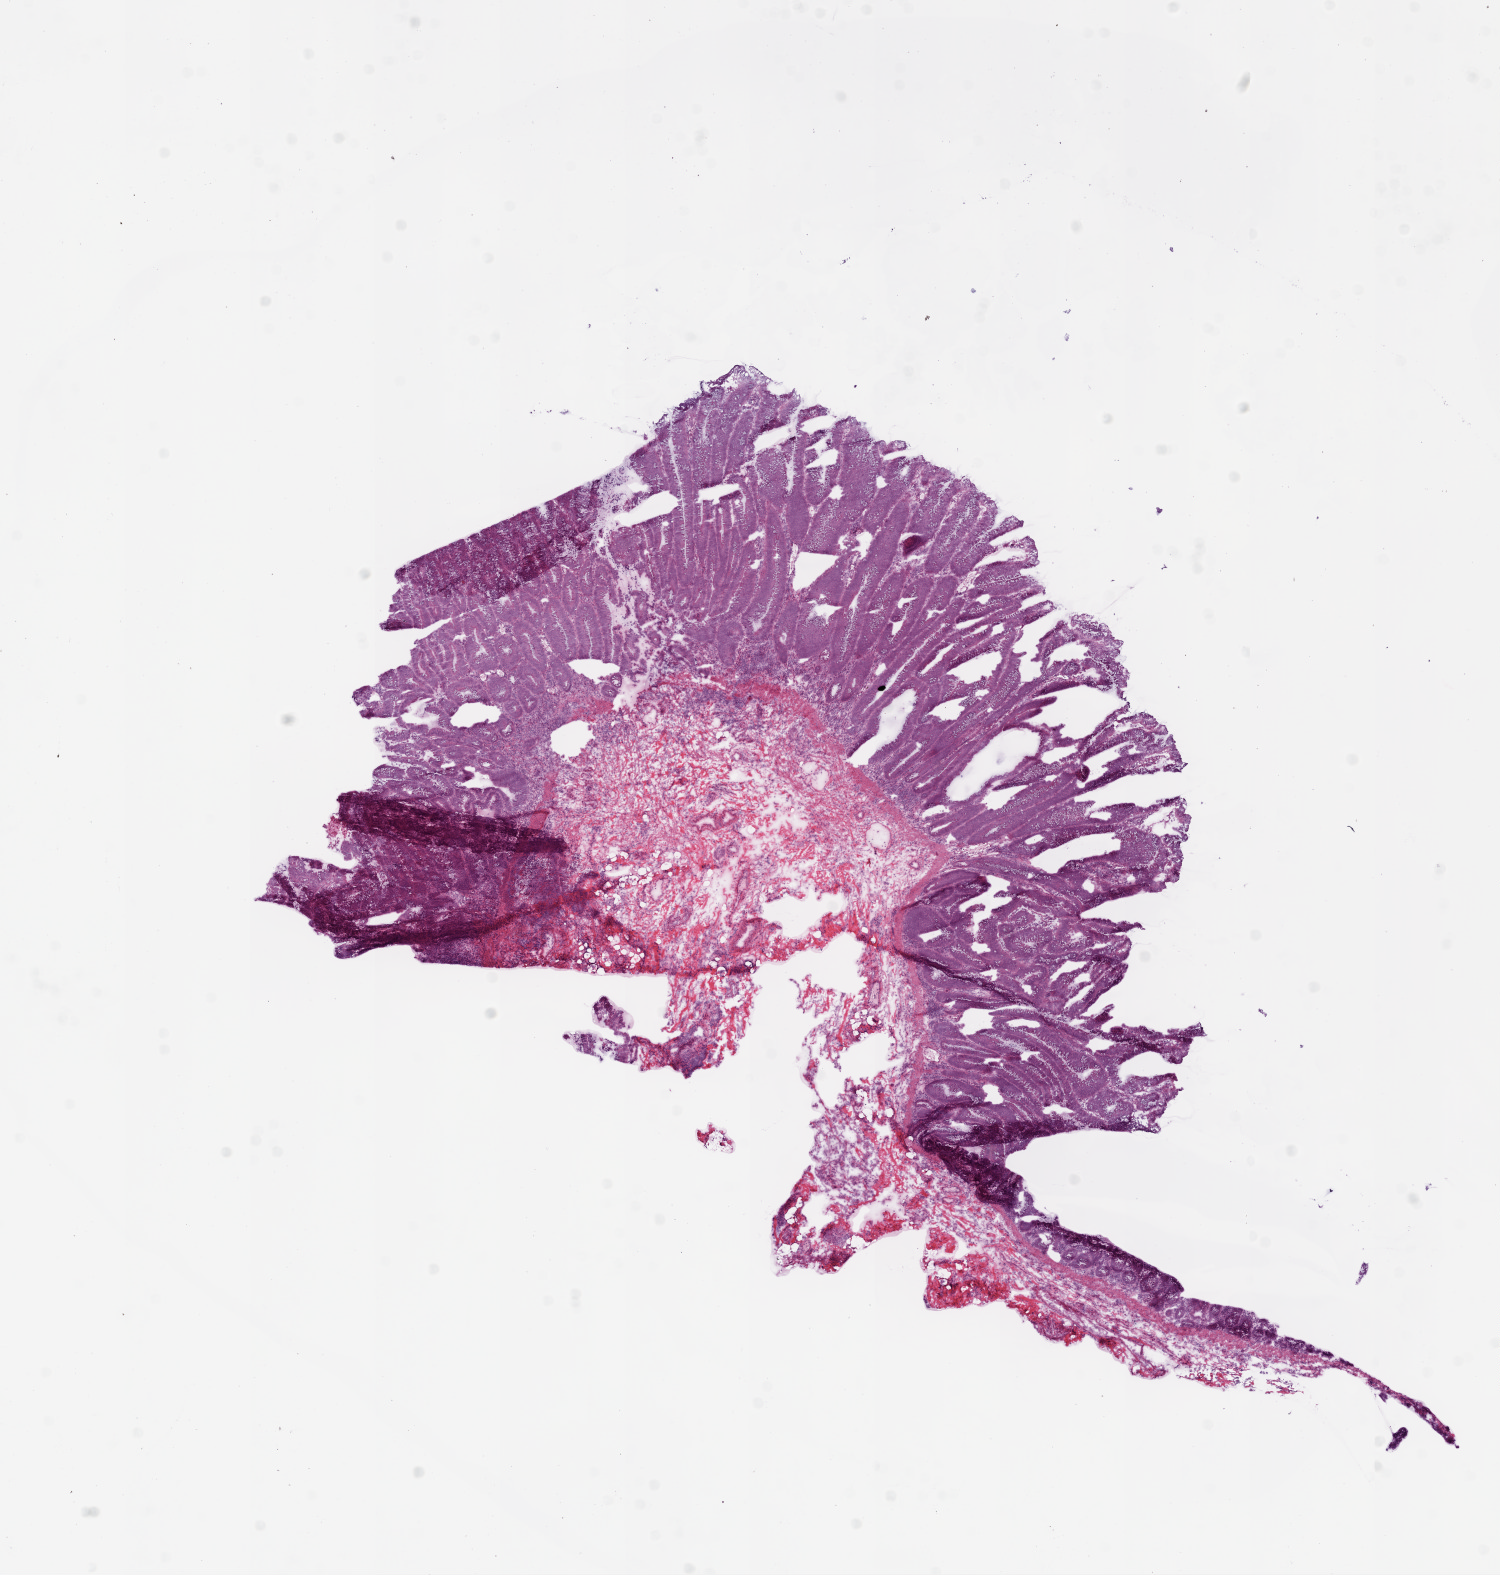
Whole-slide histology image, H&E — a low-resolution overview of the entire scanned area, about 12.0 x 12.6 mm. Frozen section from the bottom of the tissue portion. Sample: primary tumour, colon. Female, age 67 years at initial diagnosis. Slide review estimates, as recorded: tumour cells 95%, tumour nuclei 75%, normal cells 0%, stromal cells 5%, necrosis 0%.
Lymph nodes positive (case pathology): 12 of 35 examined. AJCC pathologic stage: IV (6th edition). Histologic diagnosis: Adenocarcinoma, NOS.